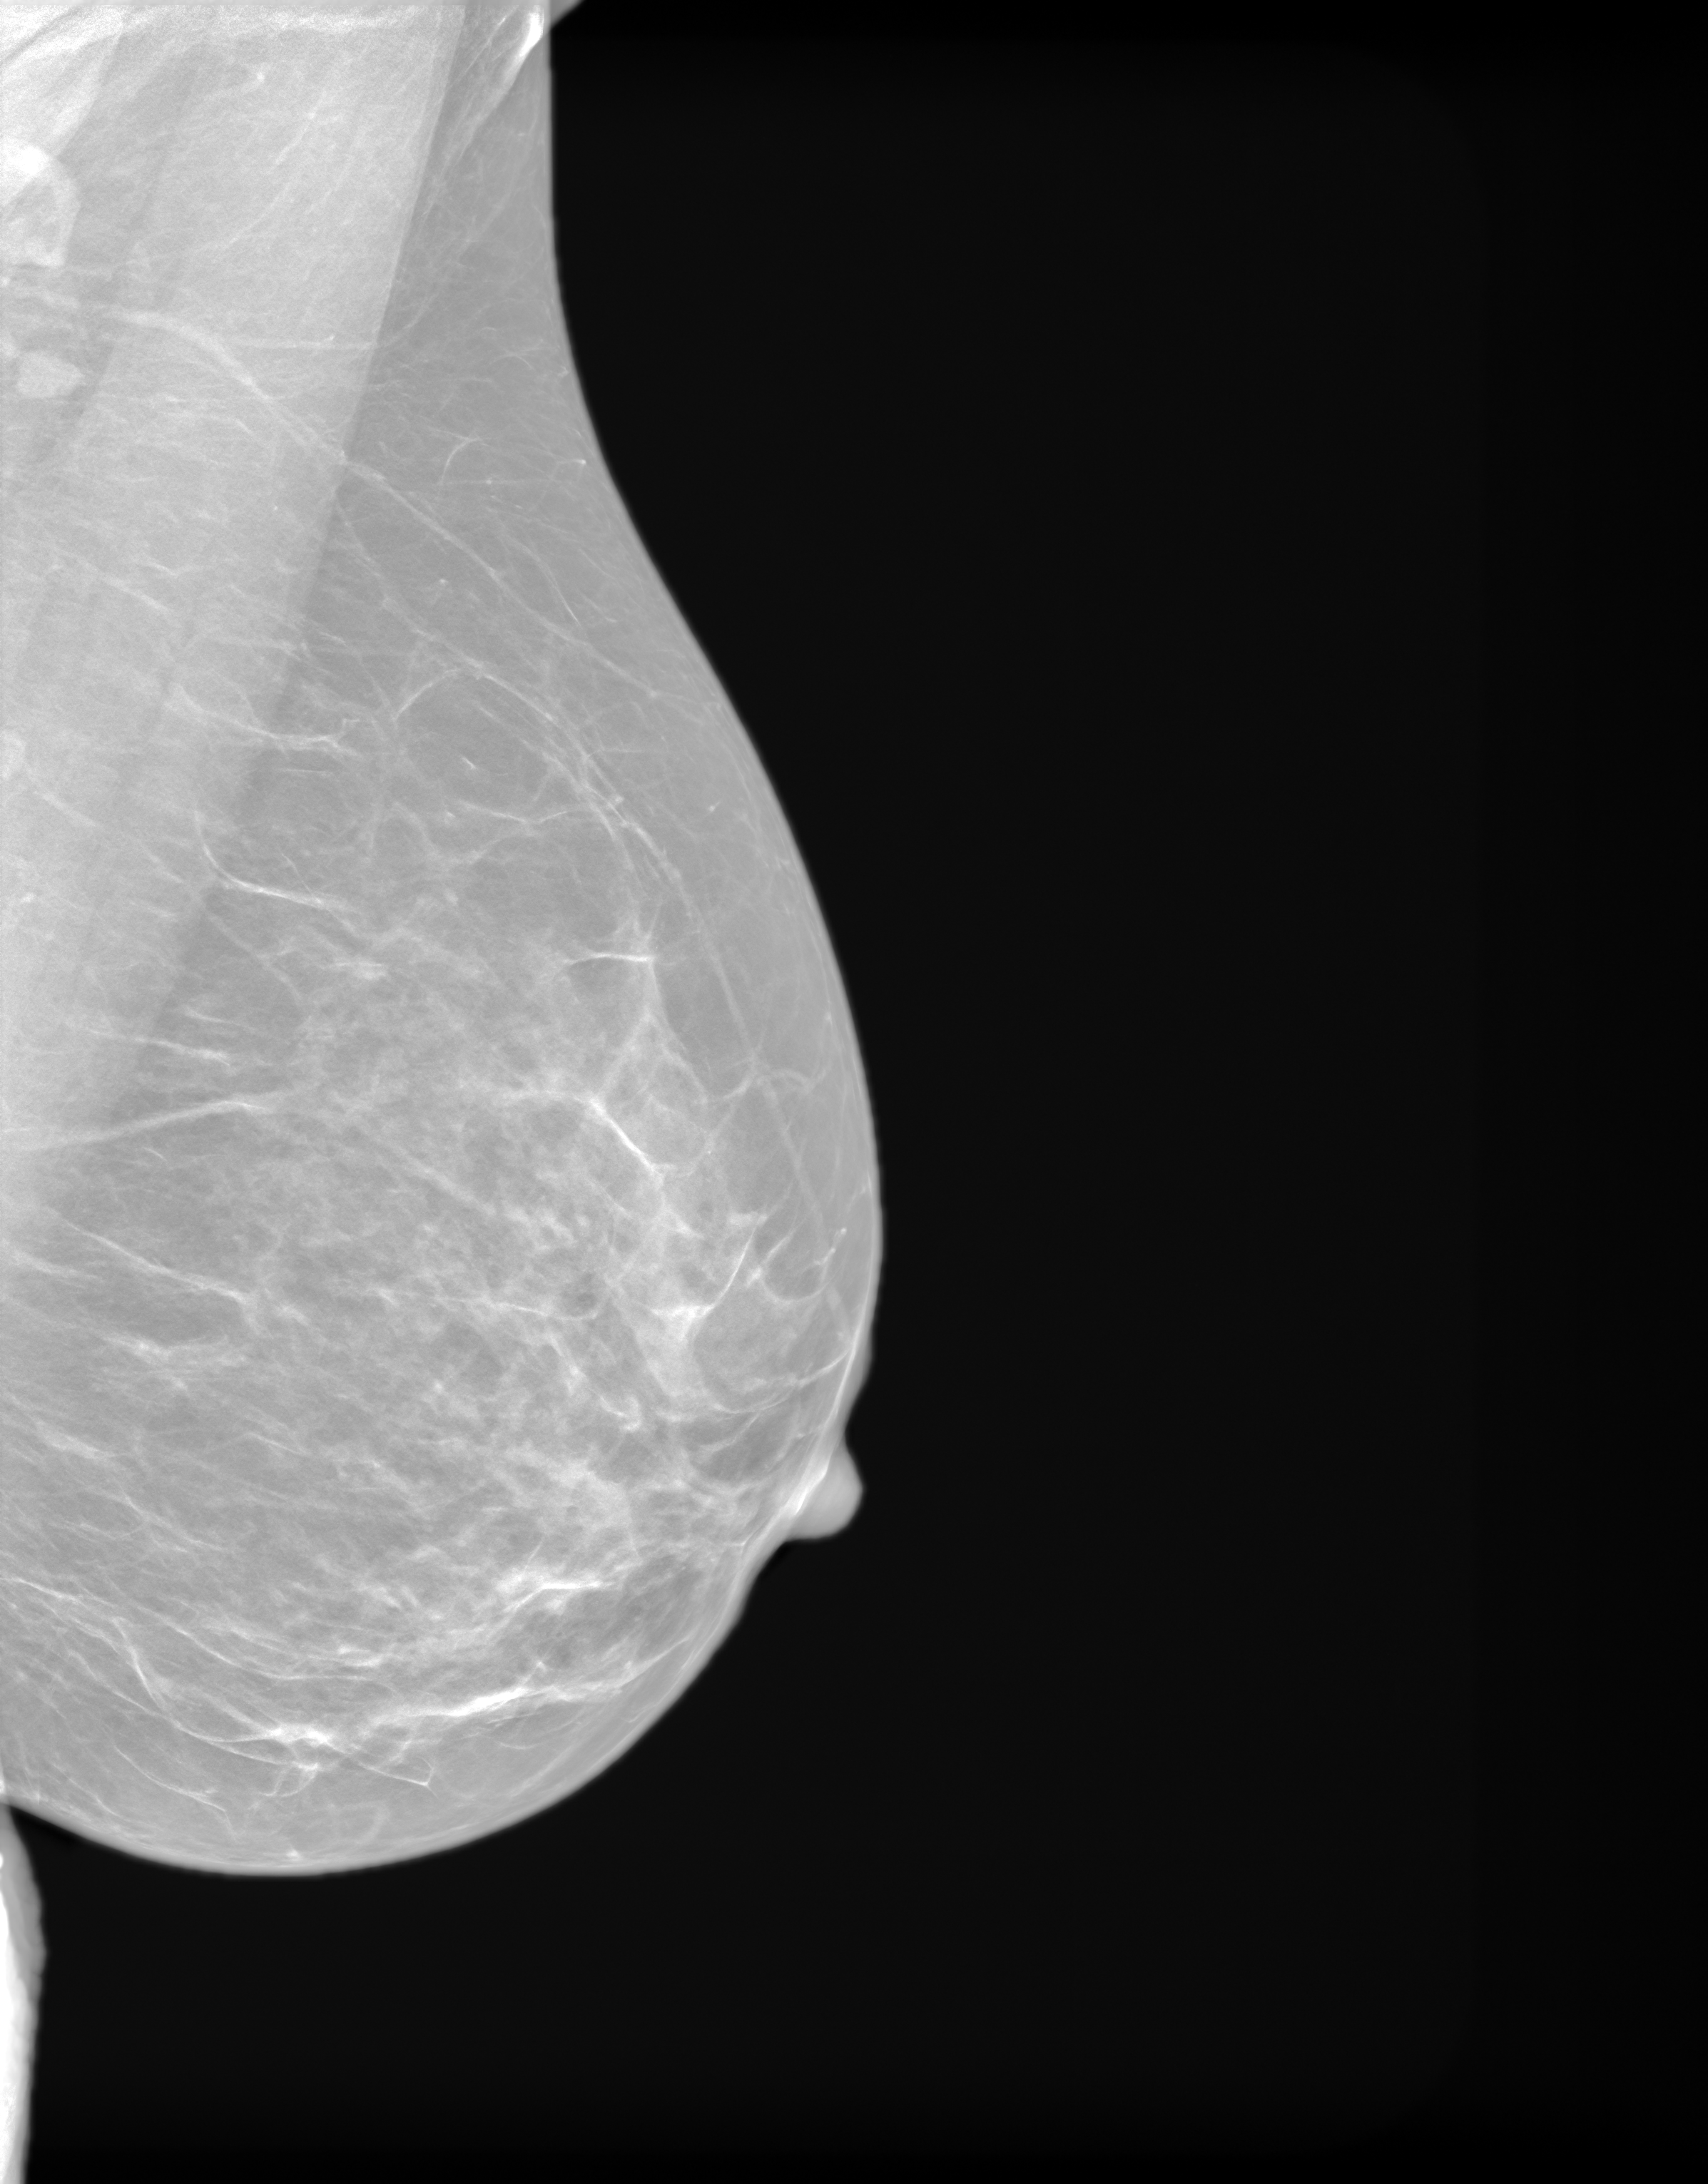
Screening examination, system: SenoIris_1SP2(440). Female patient, age 54 years.
Image type: synthesized 2-D view from tomosynthesis. Breast: left. Projection: medio-lateral oblique projection.